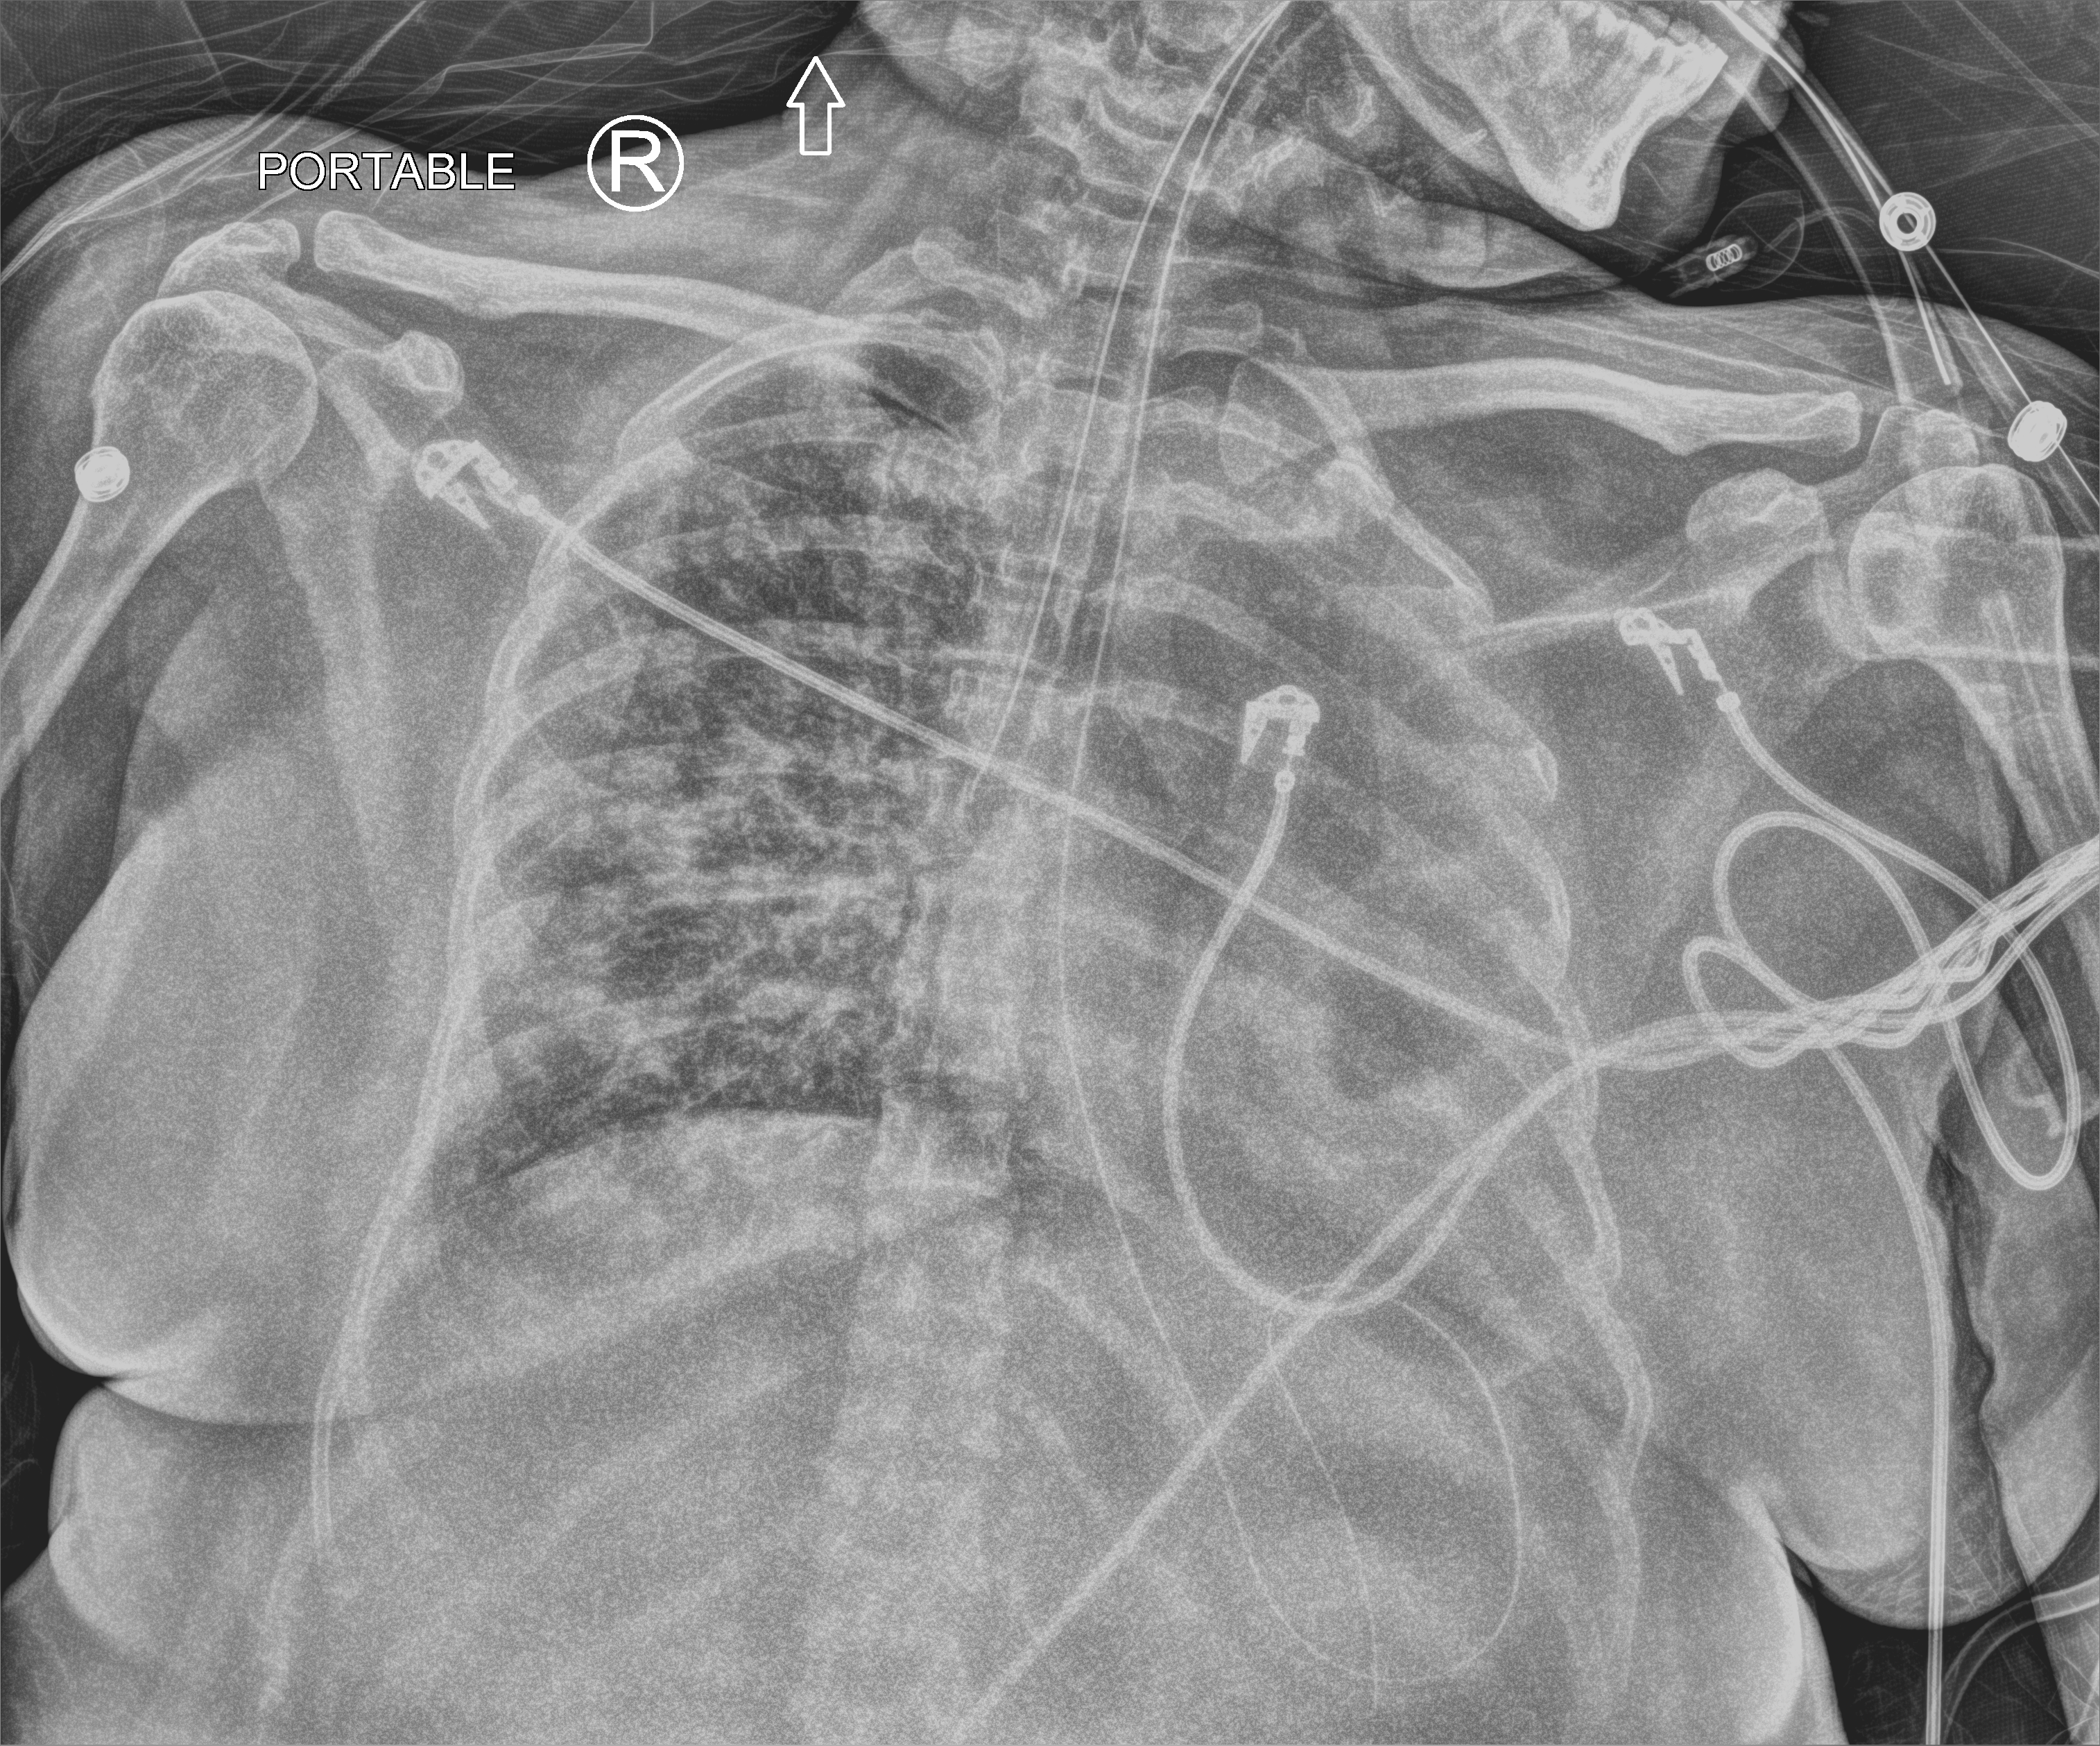
Bedside chest radiograph (computed radiography), anteroposterior (AP) projection. Adult patient hospitalised with COVID-19, age 18–59 years.
Hospital-stay facts (about this admission, not read from this image; timing relative to this image not recorded): COPD (admission record): no; admitted to intensive care during this hospital stay: yes; smoking status (admission record): never.